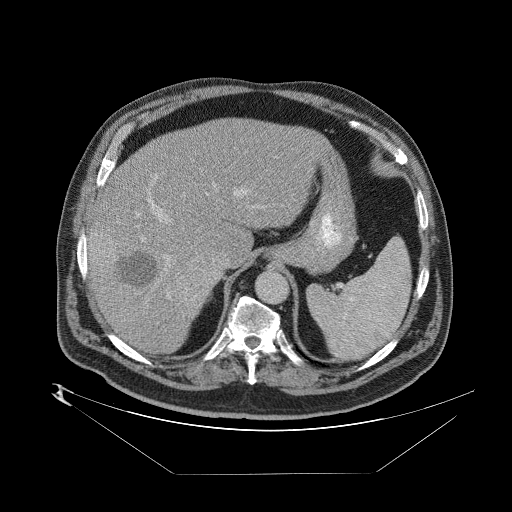
Contrast-enhanced abdominal CT (liver protocol), one axial slice. Position 59 of 89 along the scan axis. One of 2 acquisitions stored at this slice position. Soft-tissue window (W 400 / L 40 HU). 2.5 mm slice thickness. 512 × 512 image matrix, field of view 480 × 480 mm. Case-level facts recorded for this patient, not image findings: diagnosis: hepatocellular carcinoma (patient treated with transarterial chemoembolisation; whether this scan precedes or follows treatment is not stated here); TNM stage (as recorded): Stage-II; Child-Pugh class: B; tumour differentiation: moderately differentiated.
Annotated regions visible in this slice (semi-automatically segmented with operator editing):
- abdominal aorta: bounding box (x1, y1, x2, y2) in pixels: (256, 271, 288, 304)
- liver parenchyma outside the tumour (the mass and vessels are separate outlines, so this box may not span the whole liver): (88, 116, 322, 352)
- mass: (89, 236, 225, 318)
- liver vessels: (94, 173, 263, 323)